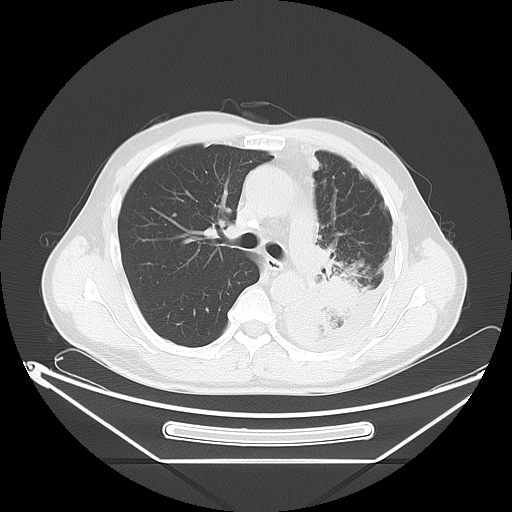
Chest CT, one axial slice. Position 40 of 63 along the scan axis. 120 kVp. Lung window (W 1500 / L -600 HU). 5 mm slice thickness. 512 × 512 image matrix, field of view 442 × 442 mm. Patient: male, 60 years. Case-level facts recorded for this patient, not image findings: clinical TNM (as recorded): T4 N1 M1.
Annotated regions visible in this slice (rectangle marked by the reading radiologist):
- lung tumour (recorded histology: adenocarcinoma): bounding box (x1, y1, x2, y2) in pixels: (303, 270, 369, 345)